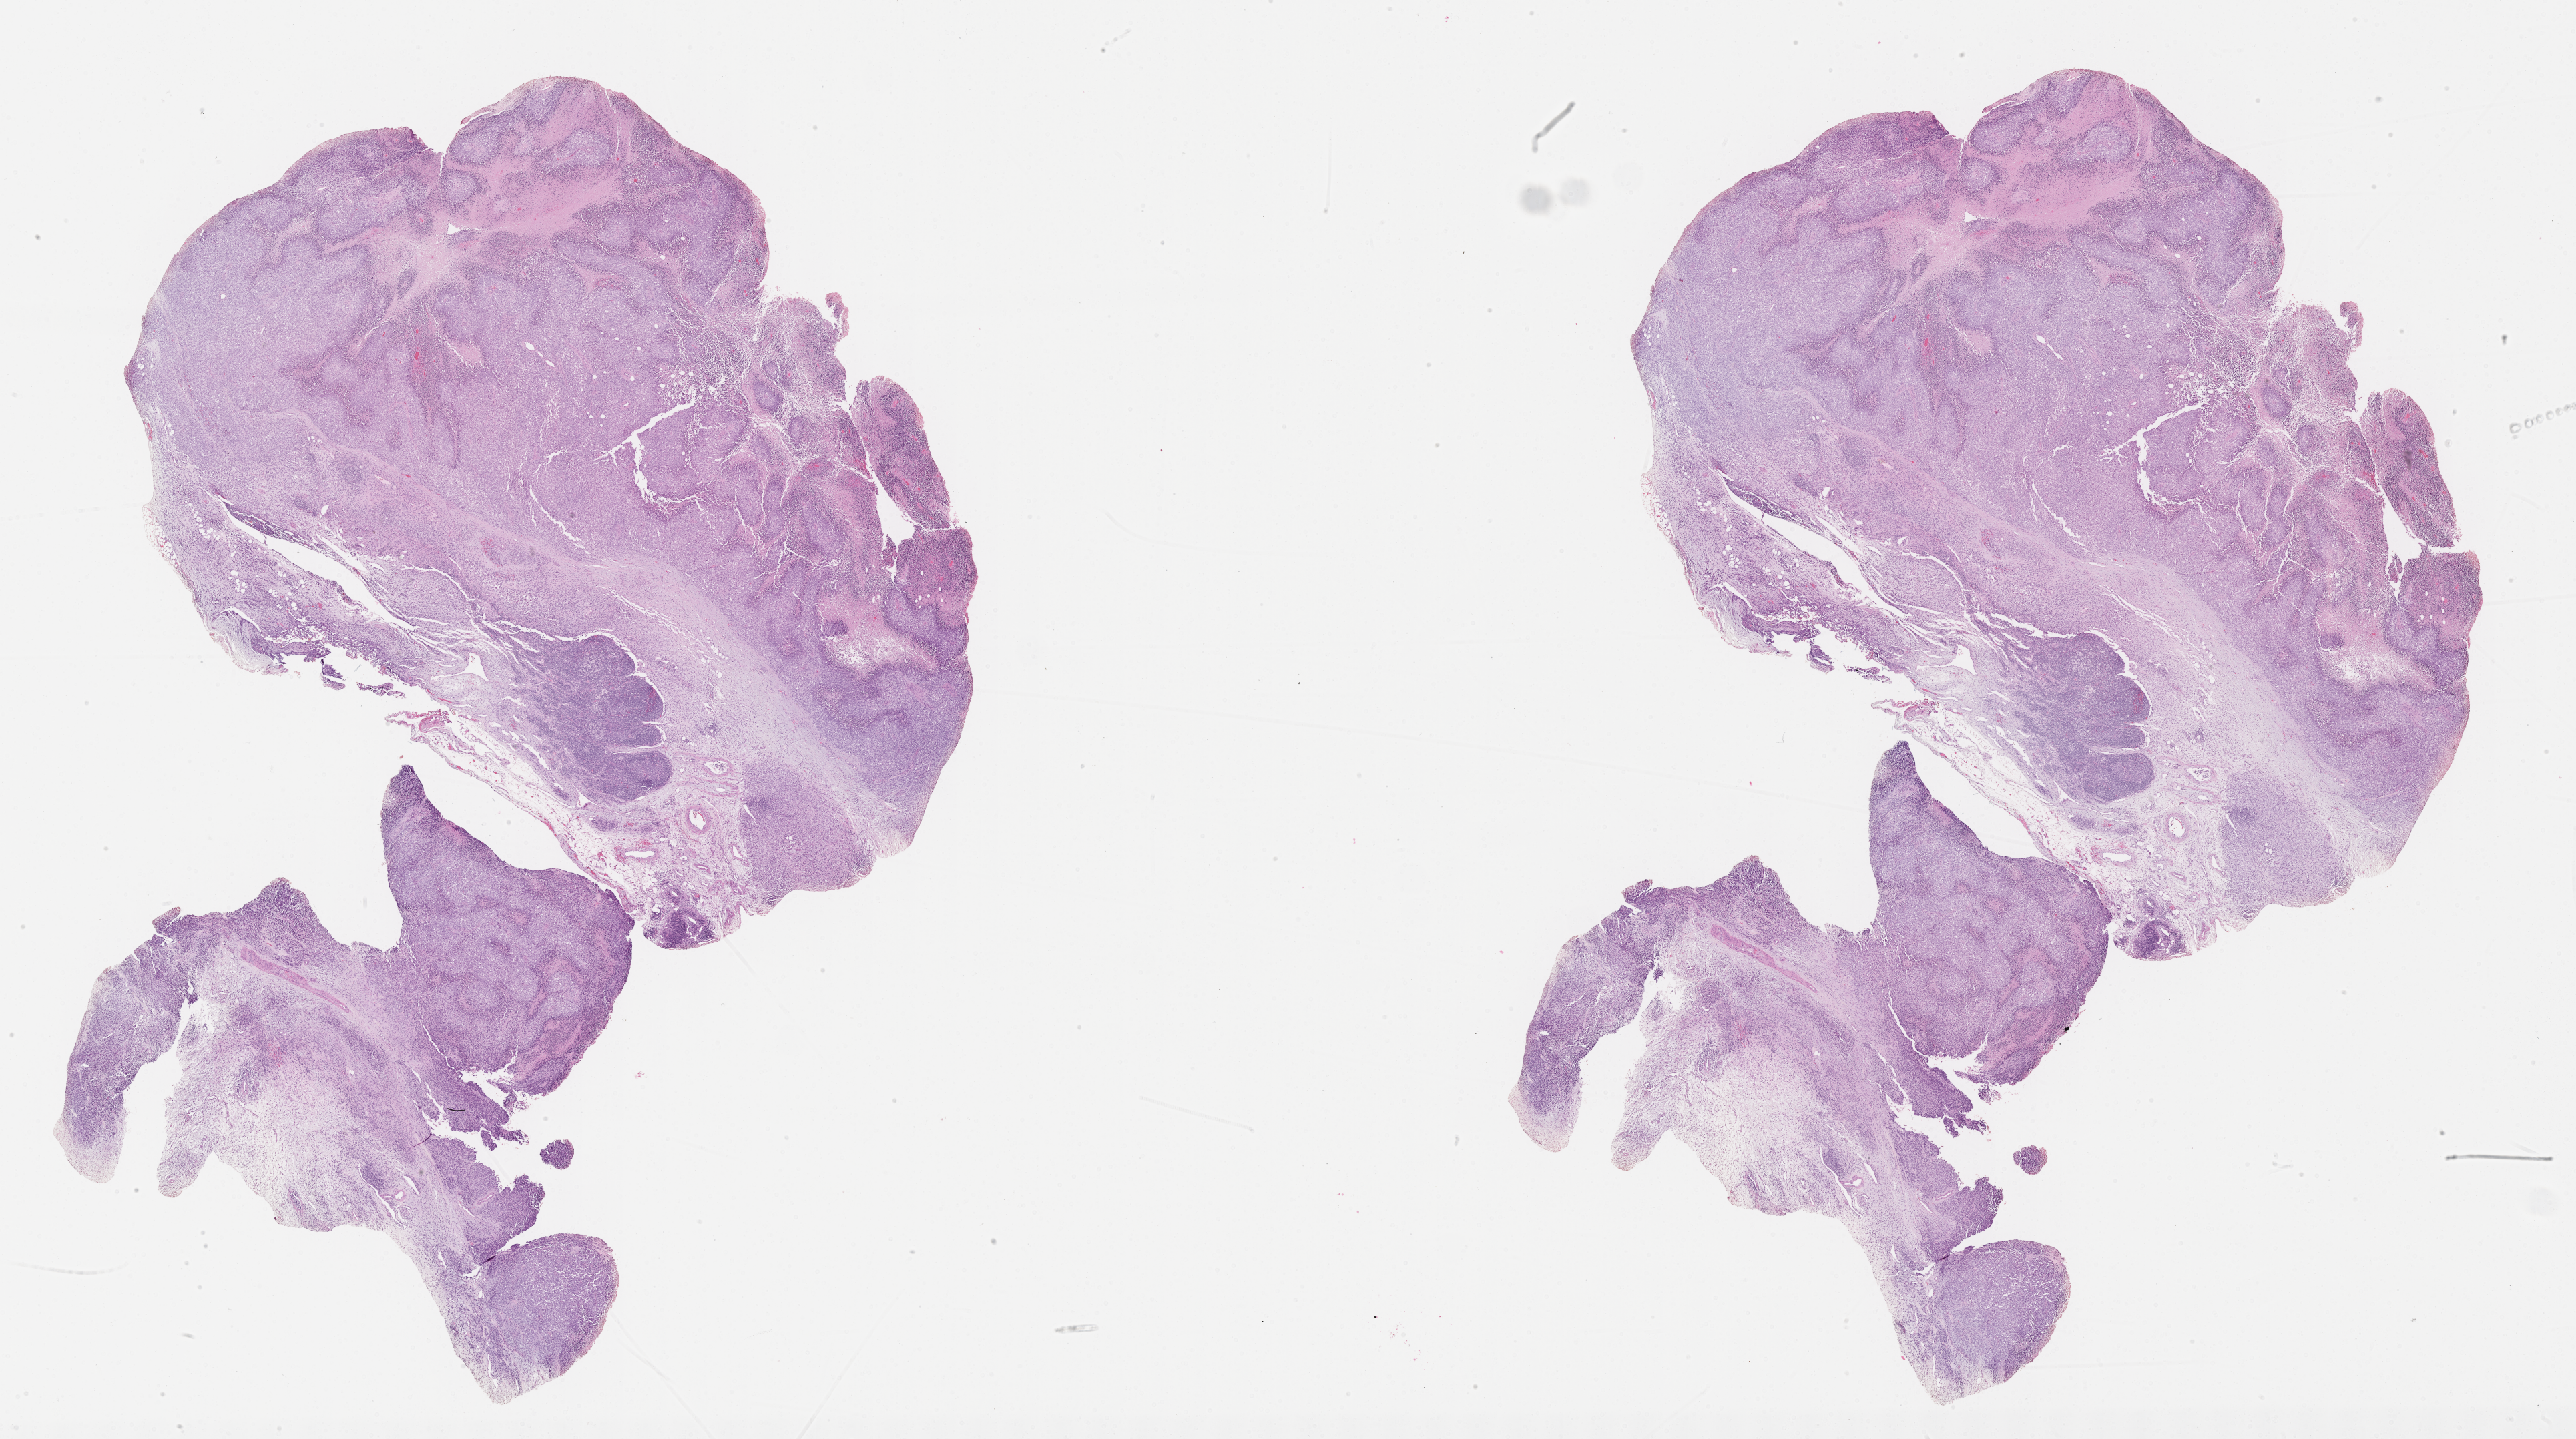
Whole-slide image, haematoxylin and eosin stain of tumor tissue, whole scanned area (about 31.2 x 17.4 mm) shown as a low-resolution overview, formalin-fixed paraffin-embedded section, site: retroperitoneum. Patient: female, age 4.1 years at diagnosis.
Stage (as recorded): 4. Diagnosis: rhabdomyosarcoma; histological classification: embryonal rhabdomyosarcoma.